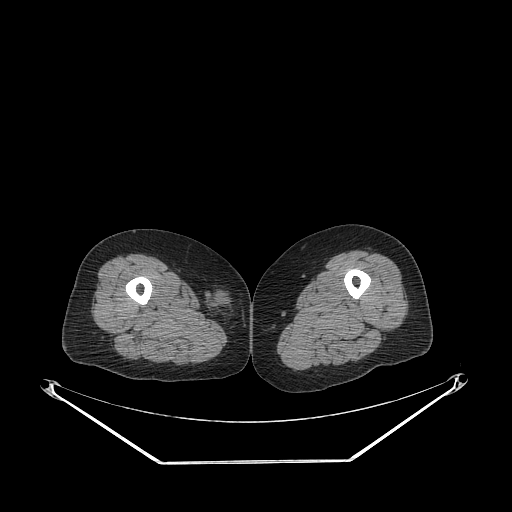
CT of an extremity soft-tissue mass (from a PET/CT study), one axial slice; position 227 of 311 along the scan axis; reconstruction kernel STANDARD; soft-tissue window (W 400 / L 40 HU); 3.75 mm slice thickness; 512 × 512 image matrix, field of view 500 × 500 mm. Female patient. Case-level facts recorded for this patient, not image findings: histological type: leiomyosarcoma; grade: intermediate; site of the primary tumour: parascapusular.
Outlined on this slice (expert contour drawn on MRI and transferred to this co-registered scan by the dataset authors):
- gross tumour volume including surrounding oedema: bounding box <210,297,231,312> (left, top, right, bottom; pixels)
- gross tumour volume (mass): <217,299,227,309>